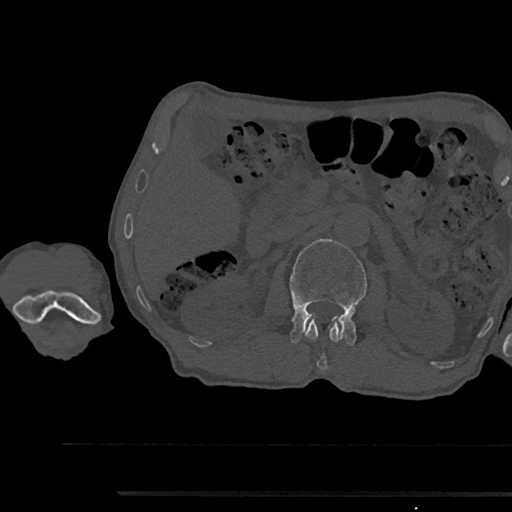
CT including the spine, one axial slice. Slice 594 of 797 in the series (ordered by position). Reconstruction kernel Br40s/3. 120 kVp. Bone window (W 1800 / L 400 HU). 0.5 mm slice thickness. 512 × 512 image matrix. Patient: male, 79 years. Case-level facts recorded for this patient, not image findings: primary cancer: prostate.
Annotated regions visible in this slice (semi-automatic segmentation, software-assisted and operator-edited):
- L1 vertebra: bounding box <305,319,342,370> (left, top, right, bottom; pixels)
- L2 vertebra: <290,239,367,345>